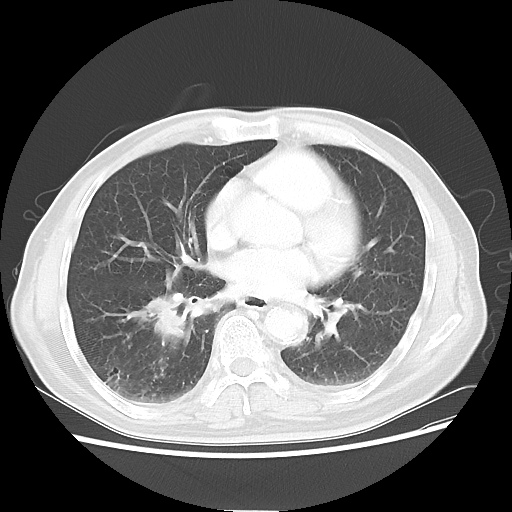
Chest CT, one axial slice; lung window (W 1500 / L -600 HU); 512 × 512 image matrix, field of view 360 × 360 mm. Male patient, age 74 years. Case-level facts recorded for this patient, not image findings: clinical TNM (as recorded): T1c N1 M1.
Structures marked on this image (rectangle marked by the reading radiologist):
- lung tumour (recorded histology: adenocarcinoma): bounding box <122,293,198,350> (left, top, right, bottom; pixels)